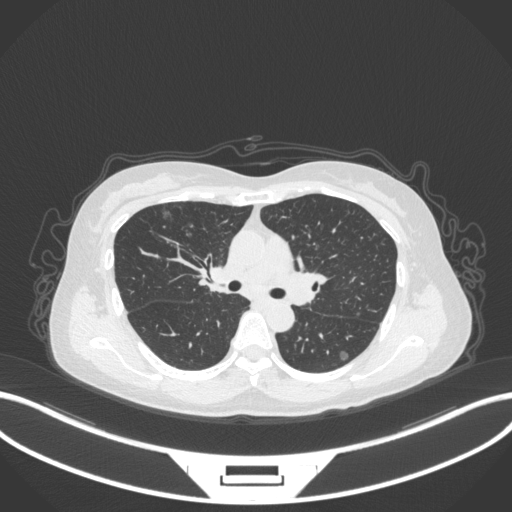
Chest CT, one axial slice. Slice 203 of 317 in the series (ordered by position). 120 kVp. Lung window (W 1500 / L -600 HU). 1 mm slice thickness. 512 × 512 image matrix, field of view 400 × 400 mm. Patient: female, 61 years. Case-level facts recorded for this patient, not image findings: clinical TNM (as recorded): T1b N0 M0; histopathological grade: G1.
Annotated regions visible in this slice (bounding box drawn by a radiologist):
- lung tumour (recorded histology: adenocarcinoma): bounding box (x1, y1, x2, y2) in pixels: (158, 207, 173, 225)